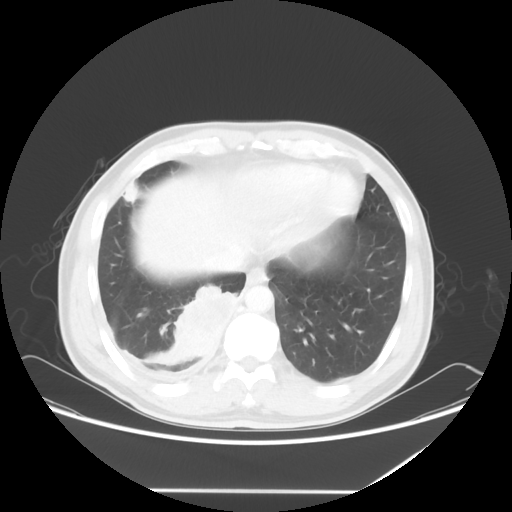
Chest CT, one axial slice. Slice 17 of 60 in the series (ordered by position). 120 kVp. Lung window (W 1500 / L -600 HU). 512 × 512 image matrix, field of view 419 × 419 mm. Male patient, age 48 years. From the clinical record (not read from this slice): clinical TNM (as recorded): T3 N3 M1a.
Annotated regions visible in this slice (bounding box drawn by a radiologist):
- lung tumour (recorded histology: squamous cell carcinoma): bounding box <173,279,240,361> (left, top, right, bottom; pixels)